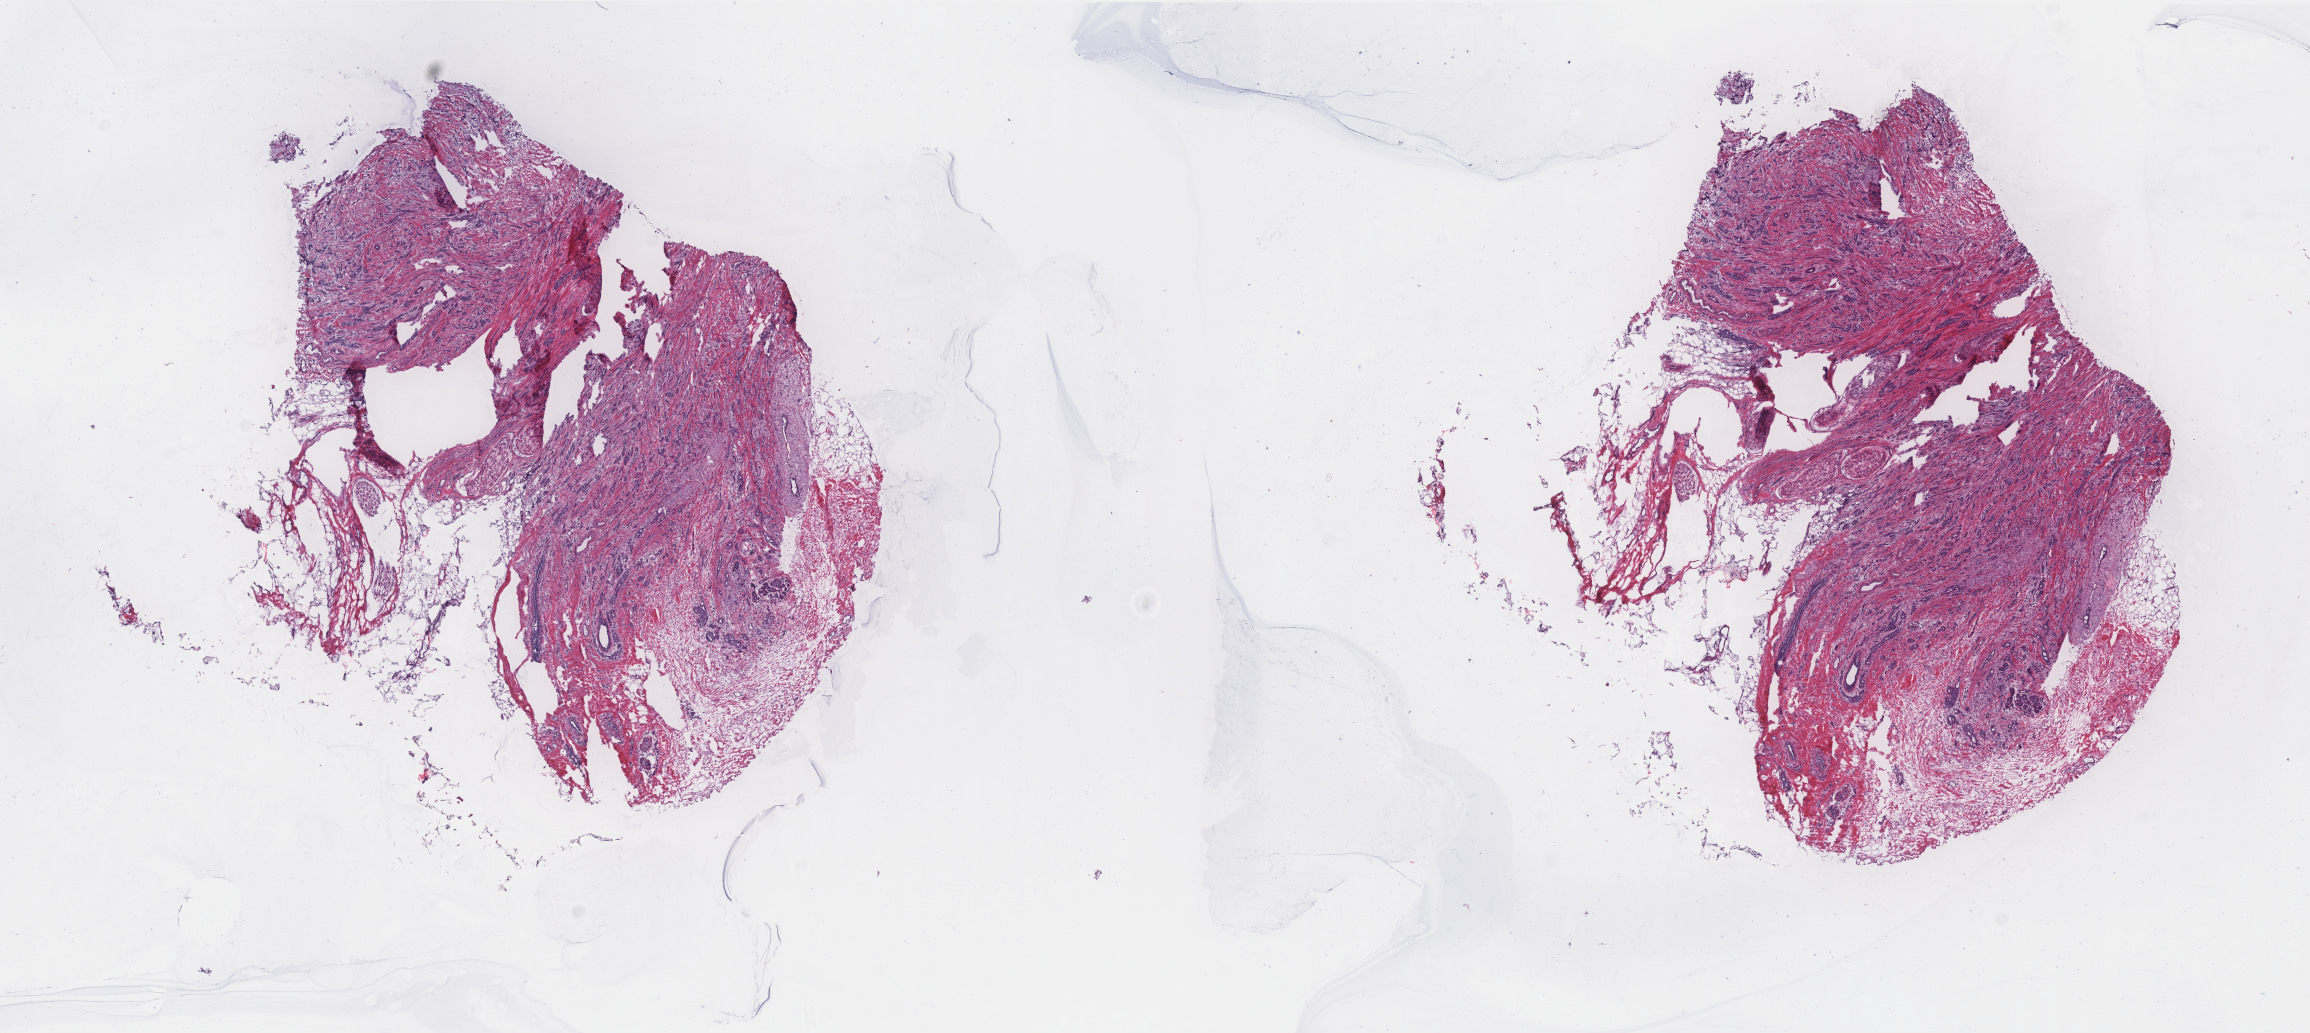
Hematoxylin and eosin (H&E) stained whole-slide image, whole scanned area (about 18.5 x 8.3 mm, from a 40x scan) shown as a low-resolution overview; frozen section from the top of the tissue portion; sample: primary tumour, breast. Female patient; age at initial diagnosis 51 years.
Pathologic diagnosis: Infiltrating duct carcinoma, NOS.